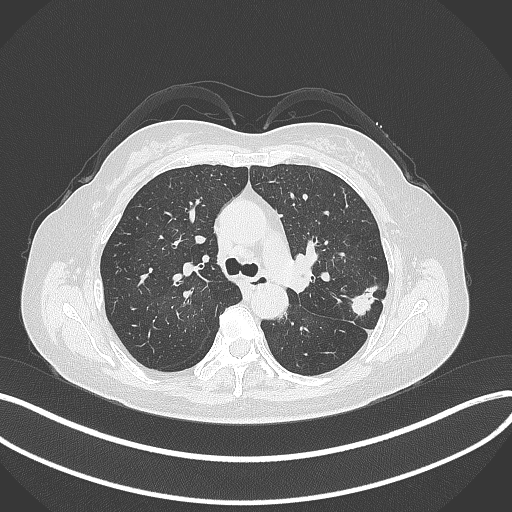
Chest CT, one axial slice; position 211 of 319 along the scan axis; 120 kVp; lung window (W 1500 / L -600 HU); 512 × 512 image matrix, field of view 400 × 400 mm. Female patient, age 60 years. From the clinical record (not read from this slice): clinical TNM (as recorded): T1c N0 M0.
Outlined on this slice (rectangle marked by the reading radiologist):
- lung tumour (recorded histology: adenocarcinoma): box from (x=349, y=280) to (x=376, y=318) px